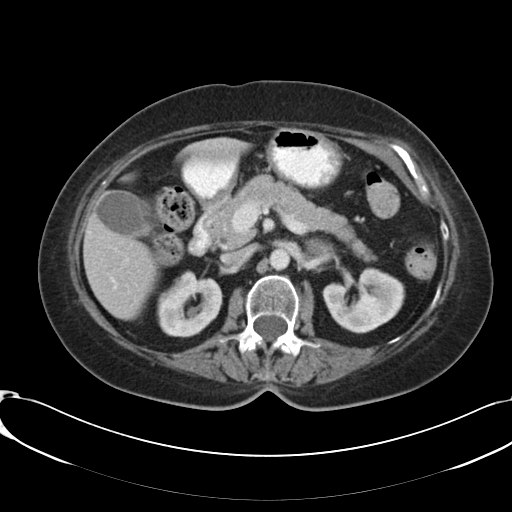
Contrast-enhanced abdominal CT, one axial slice; slice 65 of 91 in the series (ordered by position); reconstruction kernel B30f; 120 kVp; intravenous contrast given; soft-tissue window (W 400 / L 40 HU); 5 mm slice thickness; 512 × 512 image matrix. Patient: female, 73 years. Case-level facts recorded for this patient, not image findings: diagnosis: adrenocortical carcinoma; tumour side: left adrenal; tumour size at pathology: 4.9 cm; Ki-67 index: 10 %; stage (as recorded): 3.
Structures marked on this image (semi-automatic segmentation, software-assisted and operator-edited):
- mass: bounding box <307,239,330,254> (left, top, right, bottom; pixels)